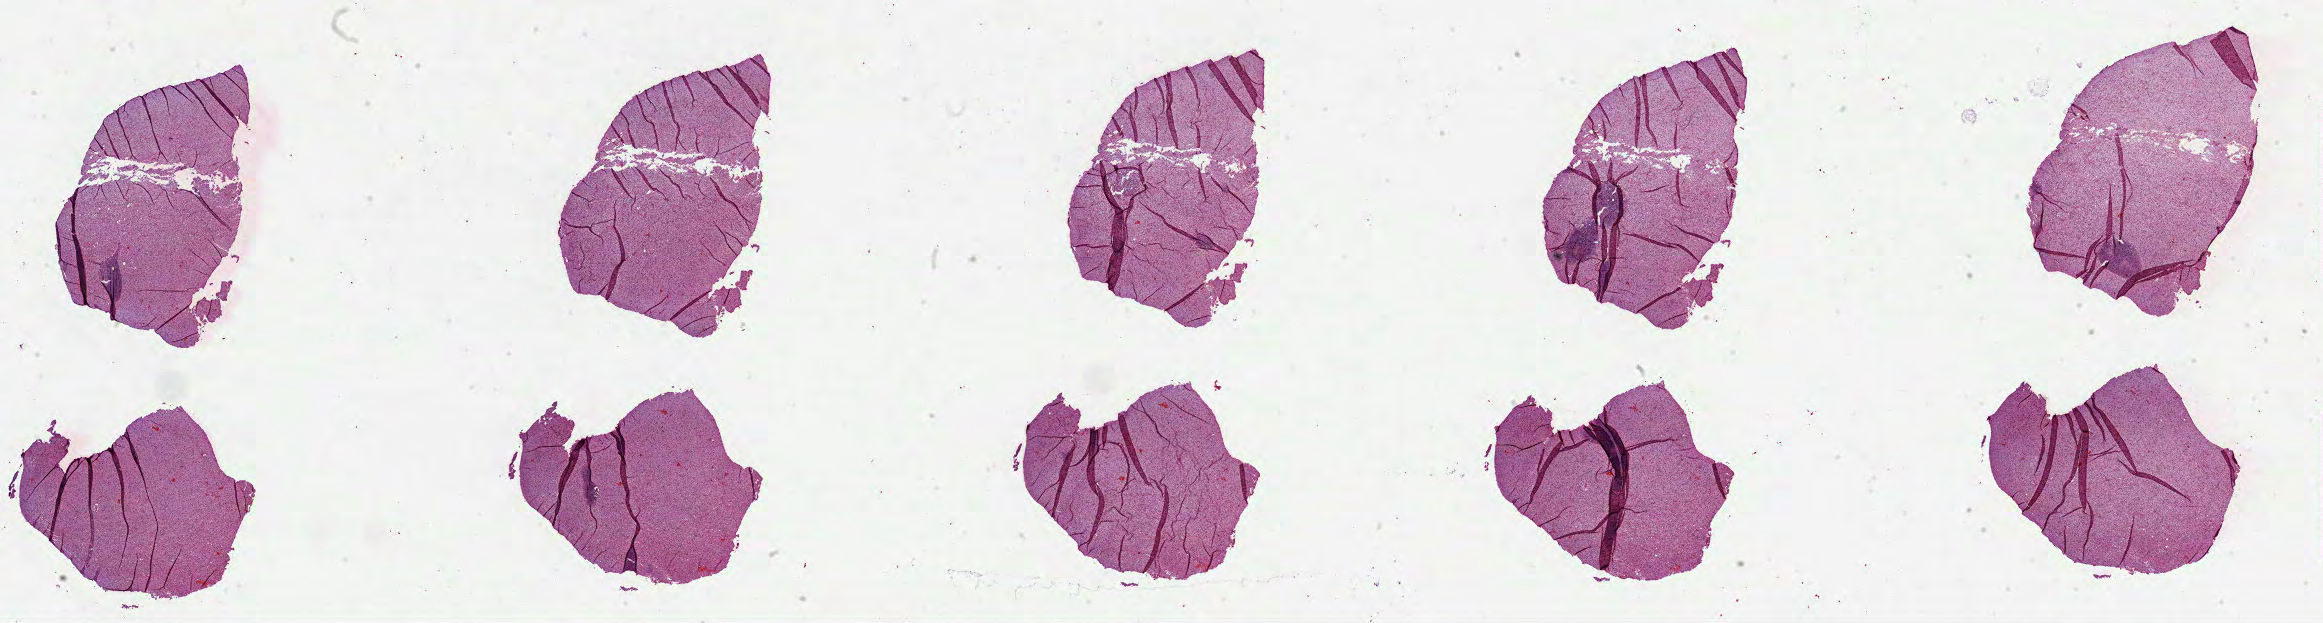
H&E whole-slide image, shown as a low-resolution overview of the whole scanned area (about 37.5 x 10.0 mm, acquisition: 40x scan); formalin-fixed paraffin-embedded (FFPE) diagnostic section; sample: primary tumour, brain. Male, age 43 years at initial diagnosis. Histologic grade: G2 (moderately differentiated).
Laterality: right. Histologic diagnosis: Mixed glioma.